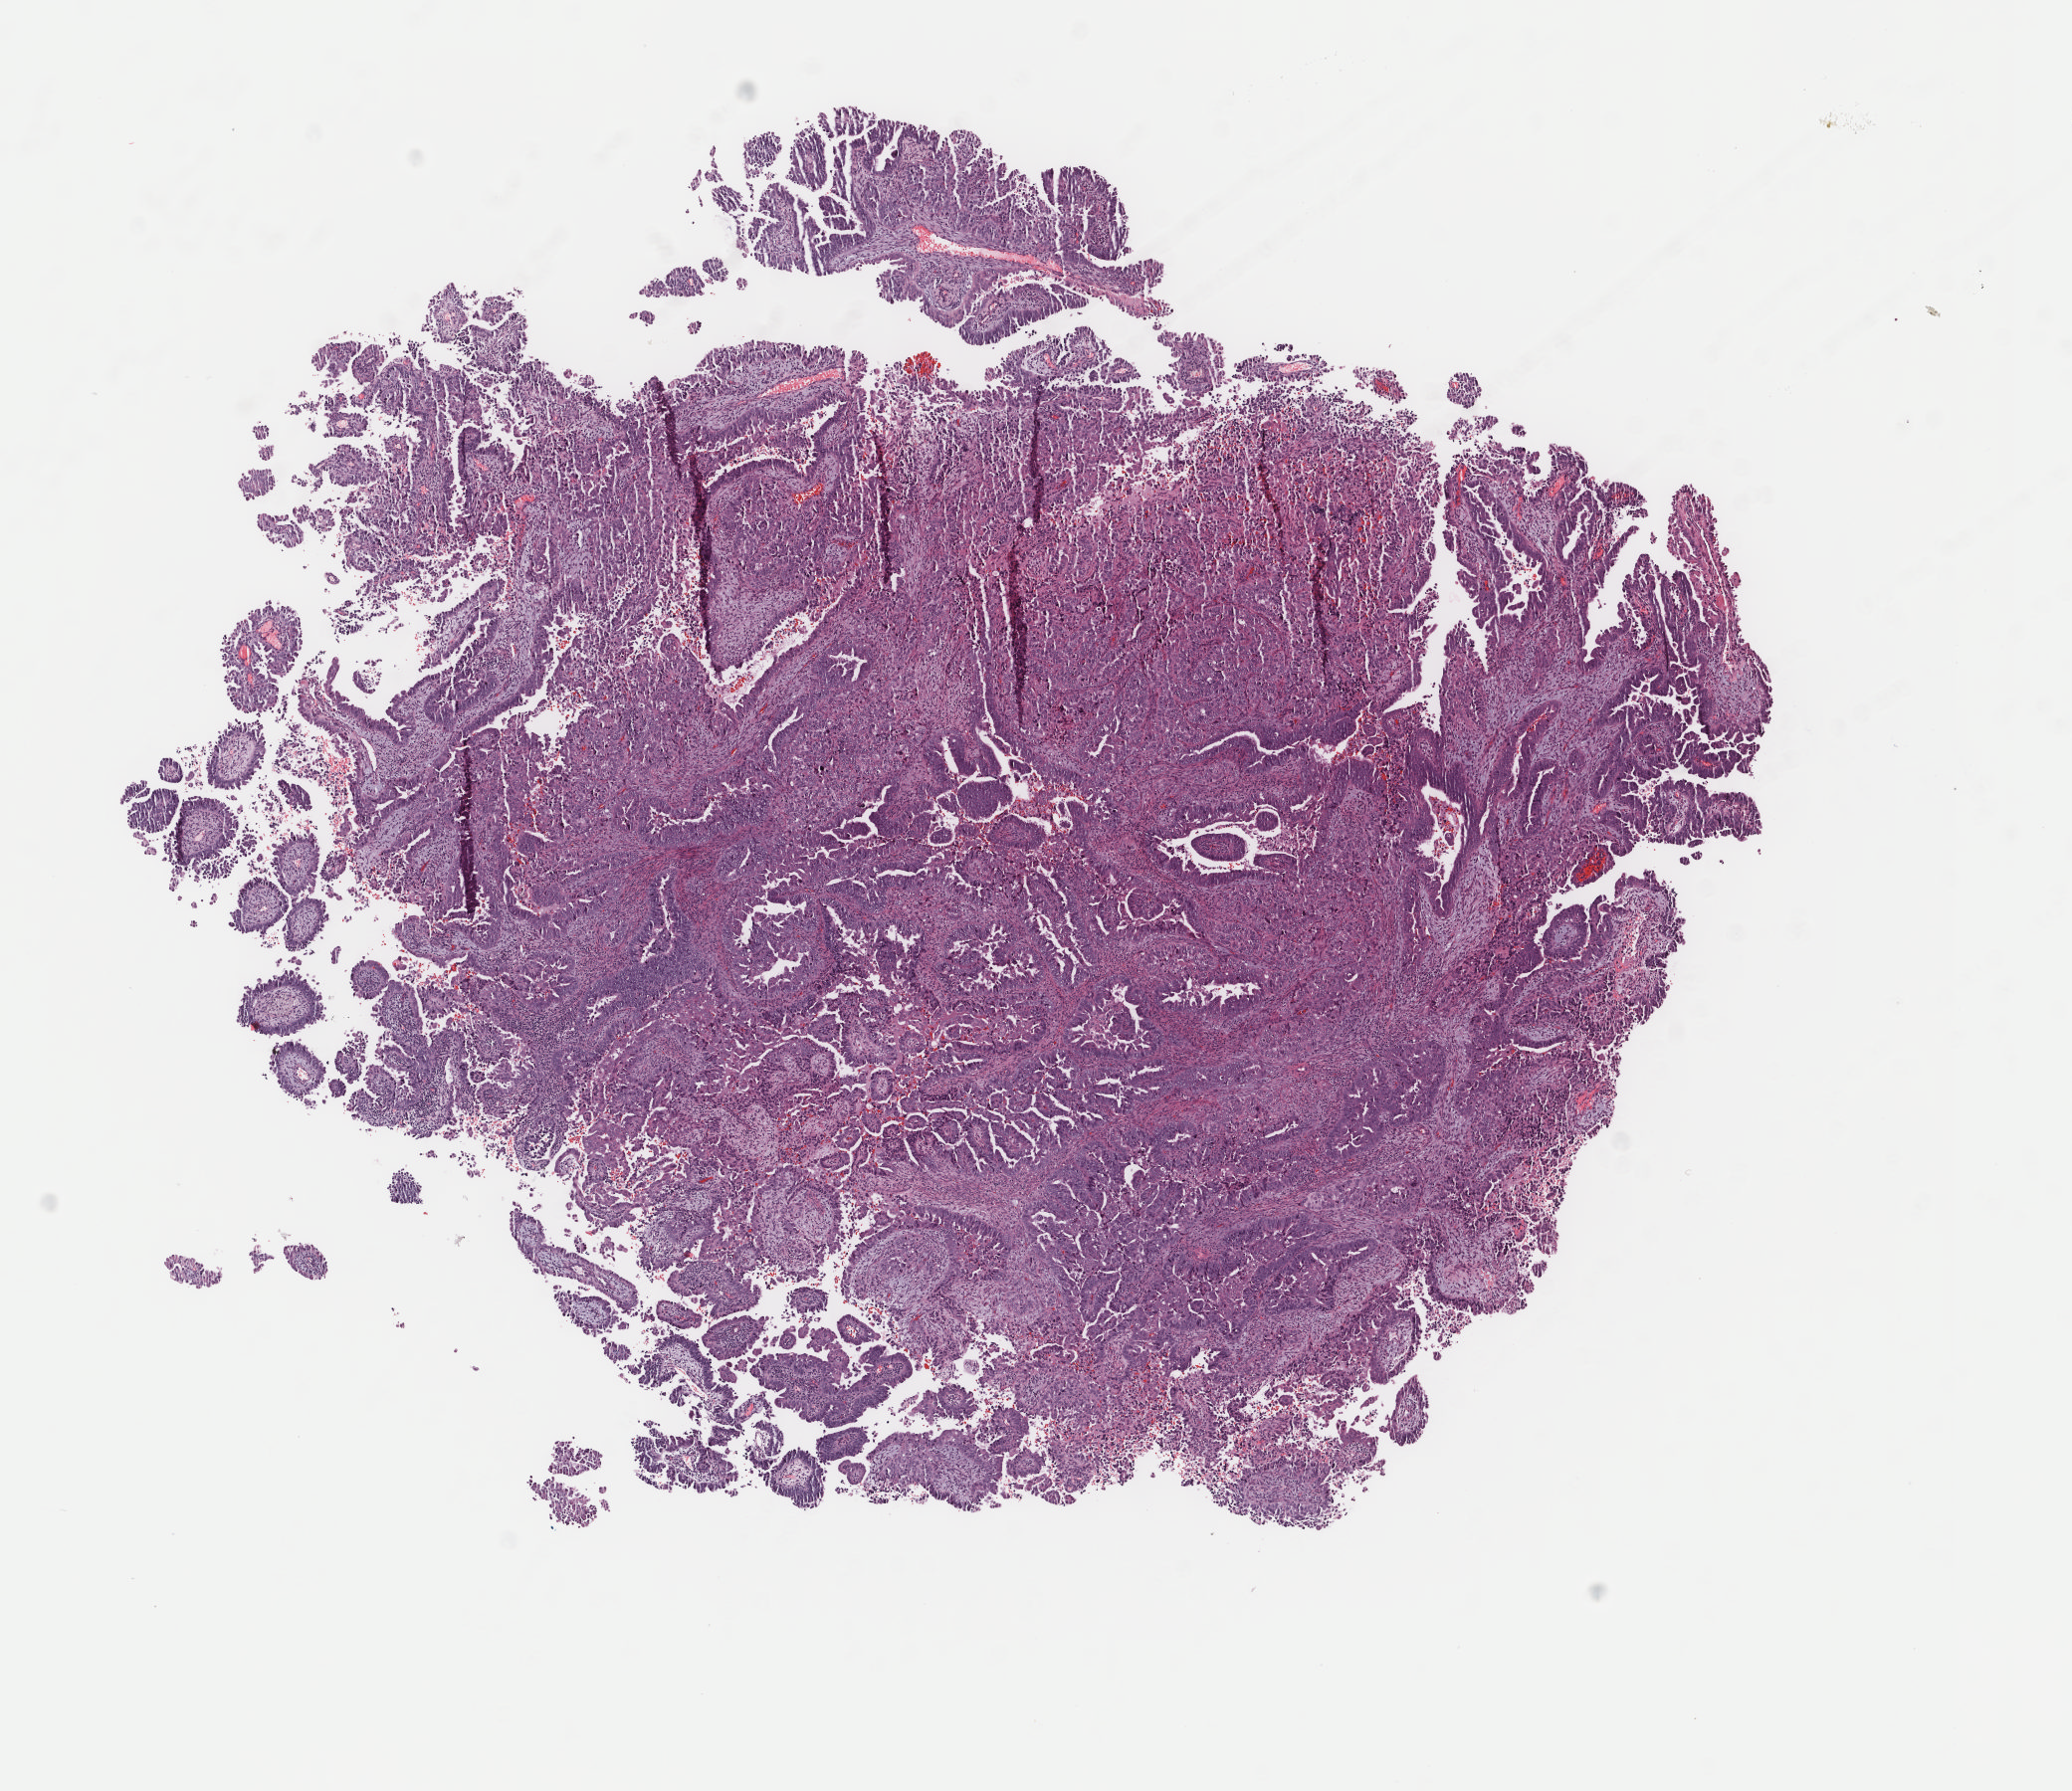
Digitized H&E tissue section (whole slide) — shown as a low-resolution overview of the whole scanned area (about 8.3 x 7.1 mm), frozen section, primary tumour sample from the uterus. Female patient; age at initial diagnosis 71 years. Histologic grade: G3 (poorly differentiated). Pathologist review of this section (percent, as recorded): tumour cells 98%, tumour nuclei 75%, normal cells 0%, stromal cells 0%, necrosis 2%. Infiltration values recorded for this section: lymphocyte infiltration 4%, monocyte infiltration 0%, neutrophil infiltration 0%.
Diagnosis: Serous cystadenocarcinoma, NOS (endometrium). FIGO stage: IIIC1.